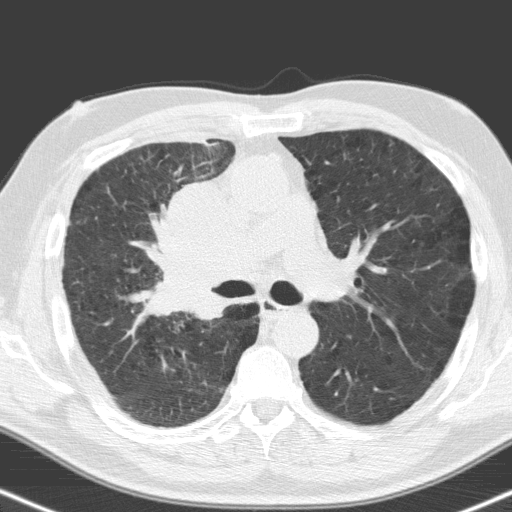
Low-dose screening chest CT, one axial slice. Slice 103 of 160 in the series (ordered by position). 120 kVp. Lung window (W 1500 / L -600 HU). 3.2 mm slice thickness. 512 × 512 image matrix, field of view 324 × 324 mm.
Outlined on this slice (outlined manually by an expert reader):
- lesion 1 (tumor, hilum of right lung): box from (x=151, y=181) to (x=260, y=318) px